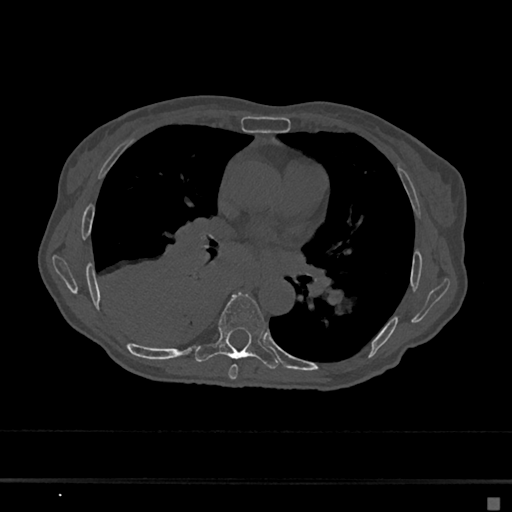
CT including the spine, one axial slice. Bone window (W 1800 / L 400 HU). 0.5 mm slice thickness. 512 × 512 image matrix. Patient: female, 68 years. Case-level facts recorded for this patient, not image findings: primary cancer: renal.
Annotated regions visible in this slice (semi-automatically segmented with operator editing):
- T6 vertebra: bounding box (x1, y1, x2, y2) in pixels: (228, 364, 238, 380)
- T7 vertebra: (195, 292, 279, 369)